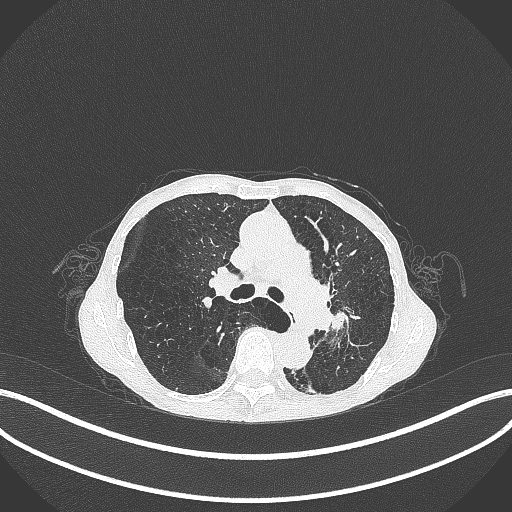
Chest CT, one axial slice; slice 176 of 347 in the series (ordered by position); reconstruction kernel B70f; 120 kVp; lung window (W 1500 / L -600 HU); 1 mm slice thickness; 512 × 512 image matrix, field of view 400 × 400 mm. Female patient, age 70 years. From the clinical record (not read from this slice): clinical TNM (as recorded): T3 N0 M0; histopathological grade: G3.
Outlined on this slice (bounding box drawn by a radiologist):
- lung tumour (recorded histology: small cell carcinoma): box from (x=329, y=300) to (x=358, y=338) px